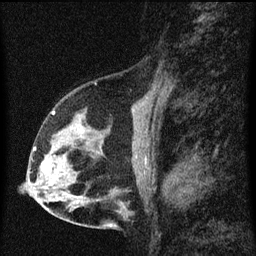
Breast MRI (dynamic contrast-enhanced), one sagittal slice; slice 36 of 60 in the series (ordered by position); dynamic contrast-enhanced series, image 2 of 3 at this slice position (ordered by acquisition); 1.5 T; TE 4.2 ms, TR 8 ms; 256 × 256 image matrix, field of view 180 × 180 mm. Patient: female, 56 years.
Annotated regions visible in this slice (semi-automatic segmentation, software-assisted and operator-edited):
- analysis volume of interest (the breast-tissue region the enhancement analysis was run in; not a lesion): bounding box [x1, y1, x2, y2] px = [34, 114, 102, 181]
- tumour enhancement mask (voxels above the 70 % enhancement threshold inside the analysis volume of interest): [34, 147, 49, 173]